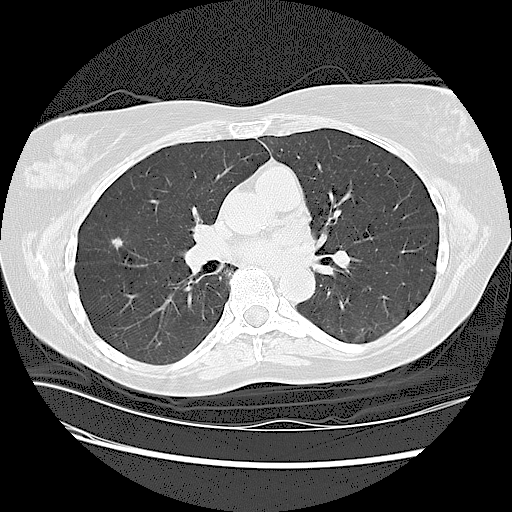
Low-dose screening chest CT, one axial slice; slice 64 of 125 in the series (ordered by position); reconstruction kernel LUNG; lung window (W 1500 / L -600 HU); 2.5 mm slice thickness; 512 × 512 image matrix, field of view 360 × 360 mm.
Structures marked on this image (expert manual segmentation):
- lesion 1 (tumor, upper lobe of right lung): bounding box <112,237,123,250> (left, top, right, bottom; pixels)